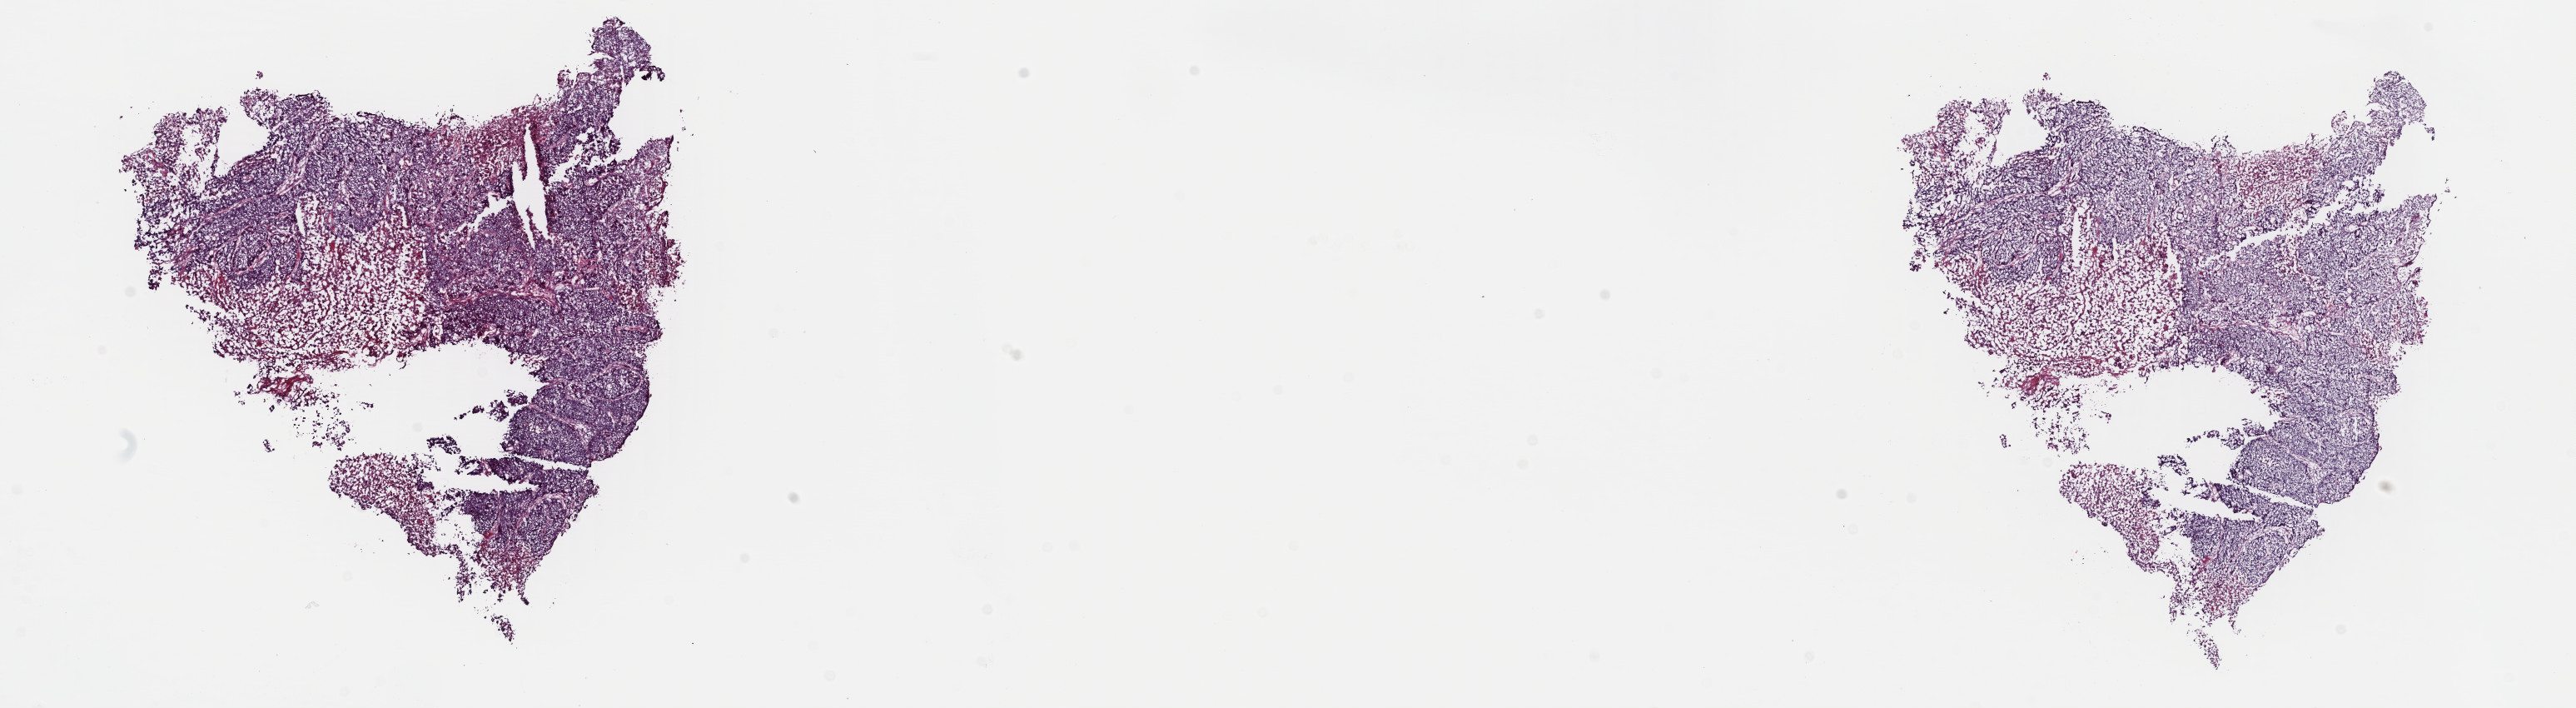
Digitized H&E-stained tissue section (whole slide), shown as a low-resolution overview of the whole scanned area (about 24.4 x 6.7 mm); frozen section from the top of the tissue portion; primary tumour sample from the lung. Male patient; age at initial diagnosis 54 years. Composition of this section per pathologist review: tumour cells 75%, tumour nuclei 100%, normal cells 0%, stromal cells 5%, necrosis 20%. Infiltration values recorded for this section: lymphocyte infiltration 1%, monocyte infiltration 1%, neutrophil infiltration 4%.
TNM: T2a N0 MX. Pathologic diagnosis: Squamous cell carcinoma, keratinizing, NOS (upper lobe, lung). AJCC pathologic stage: IB (7th edition).